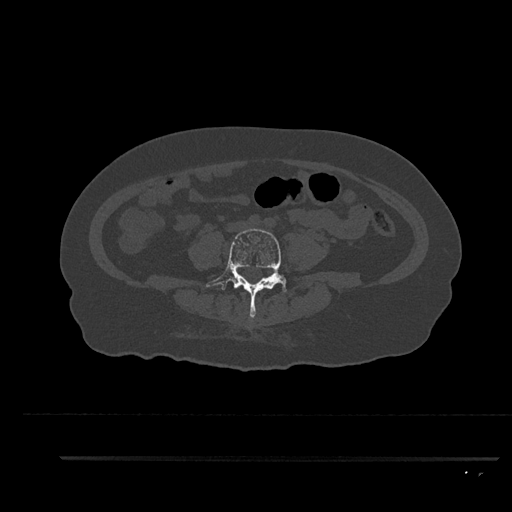
CT including the spine, one axial slice; slice 20 of 797 in the series (ordered by position); reconstruction kernel Br40s/3; bone window (W 1800 / L 400 HU); 0.5 mm slice thickness; 512 × 512 image matrix, field of view 408 × 408 mm. Patient: female, 44 years. Case-level facts recorded for this patient, not image findings: primary cancer: renal.
Annotated regions visible in this slice (semi-automatic segmentation, software-assisted and operator-edited):
- L4 vertebra: box from (x=206, y=228) to (x=287, y=318) px